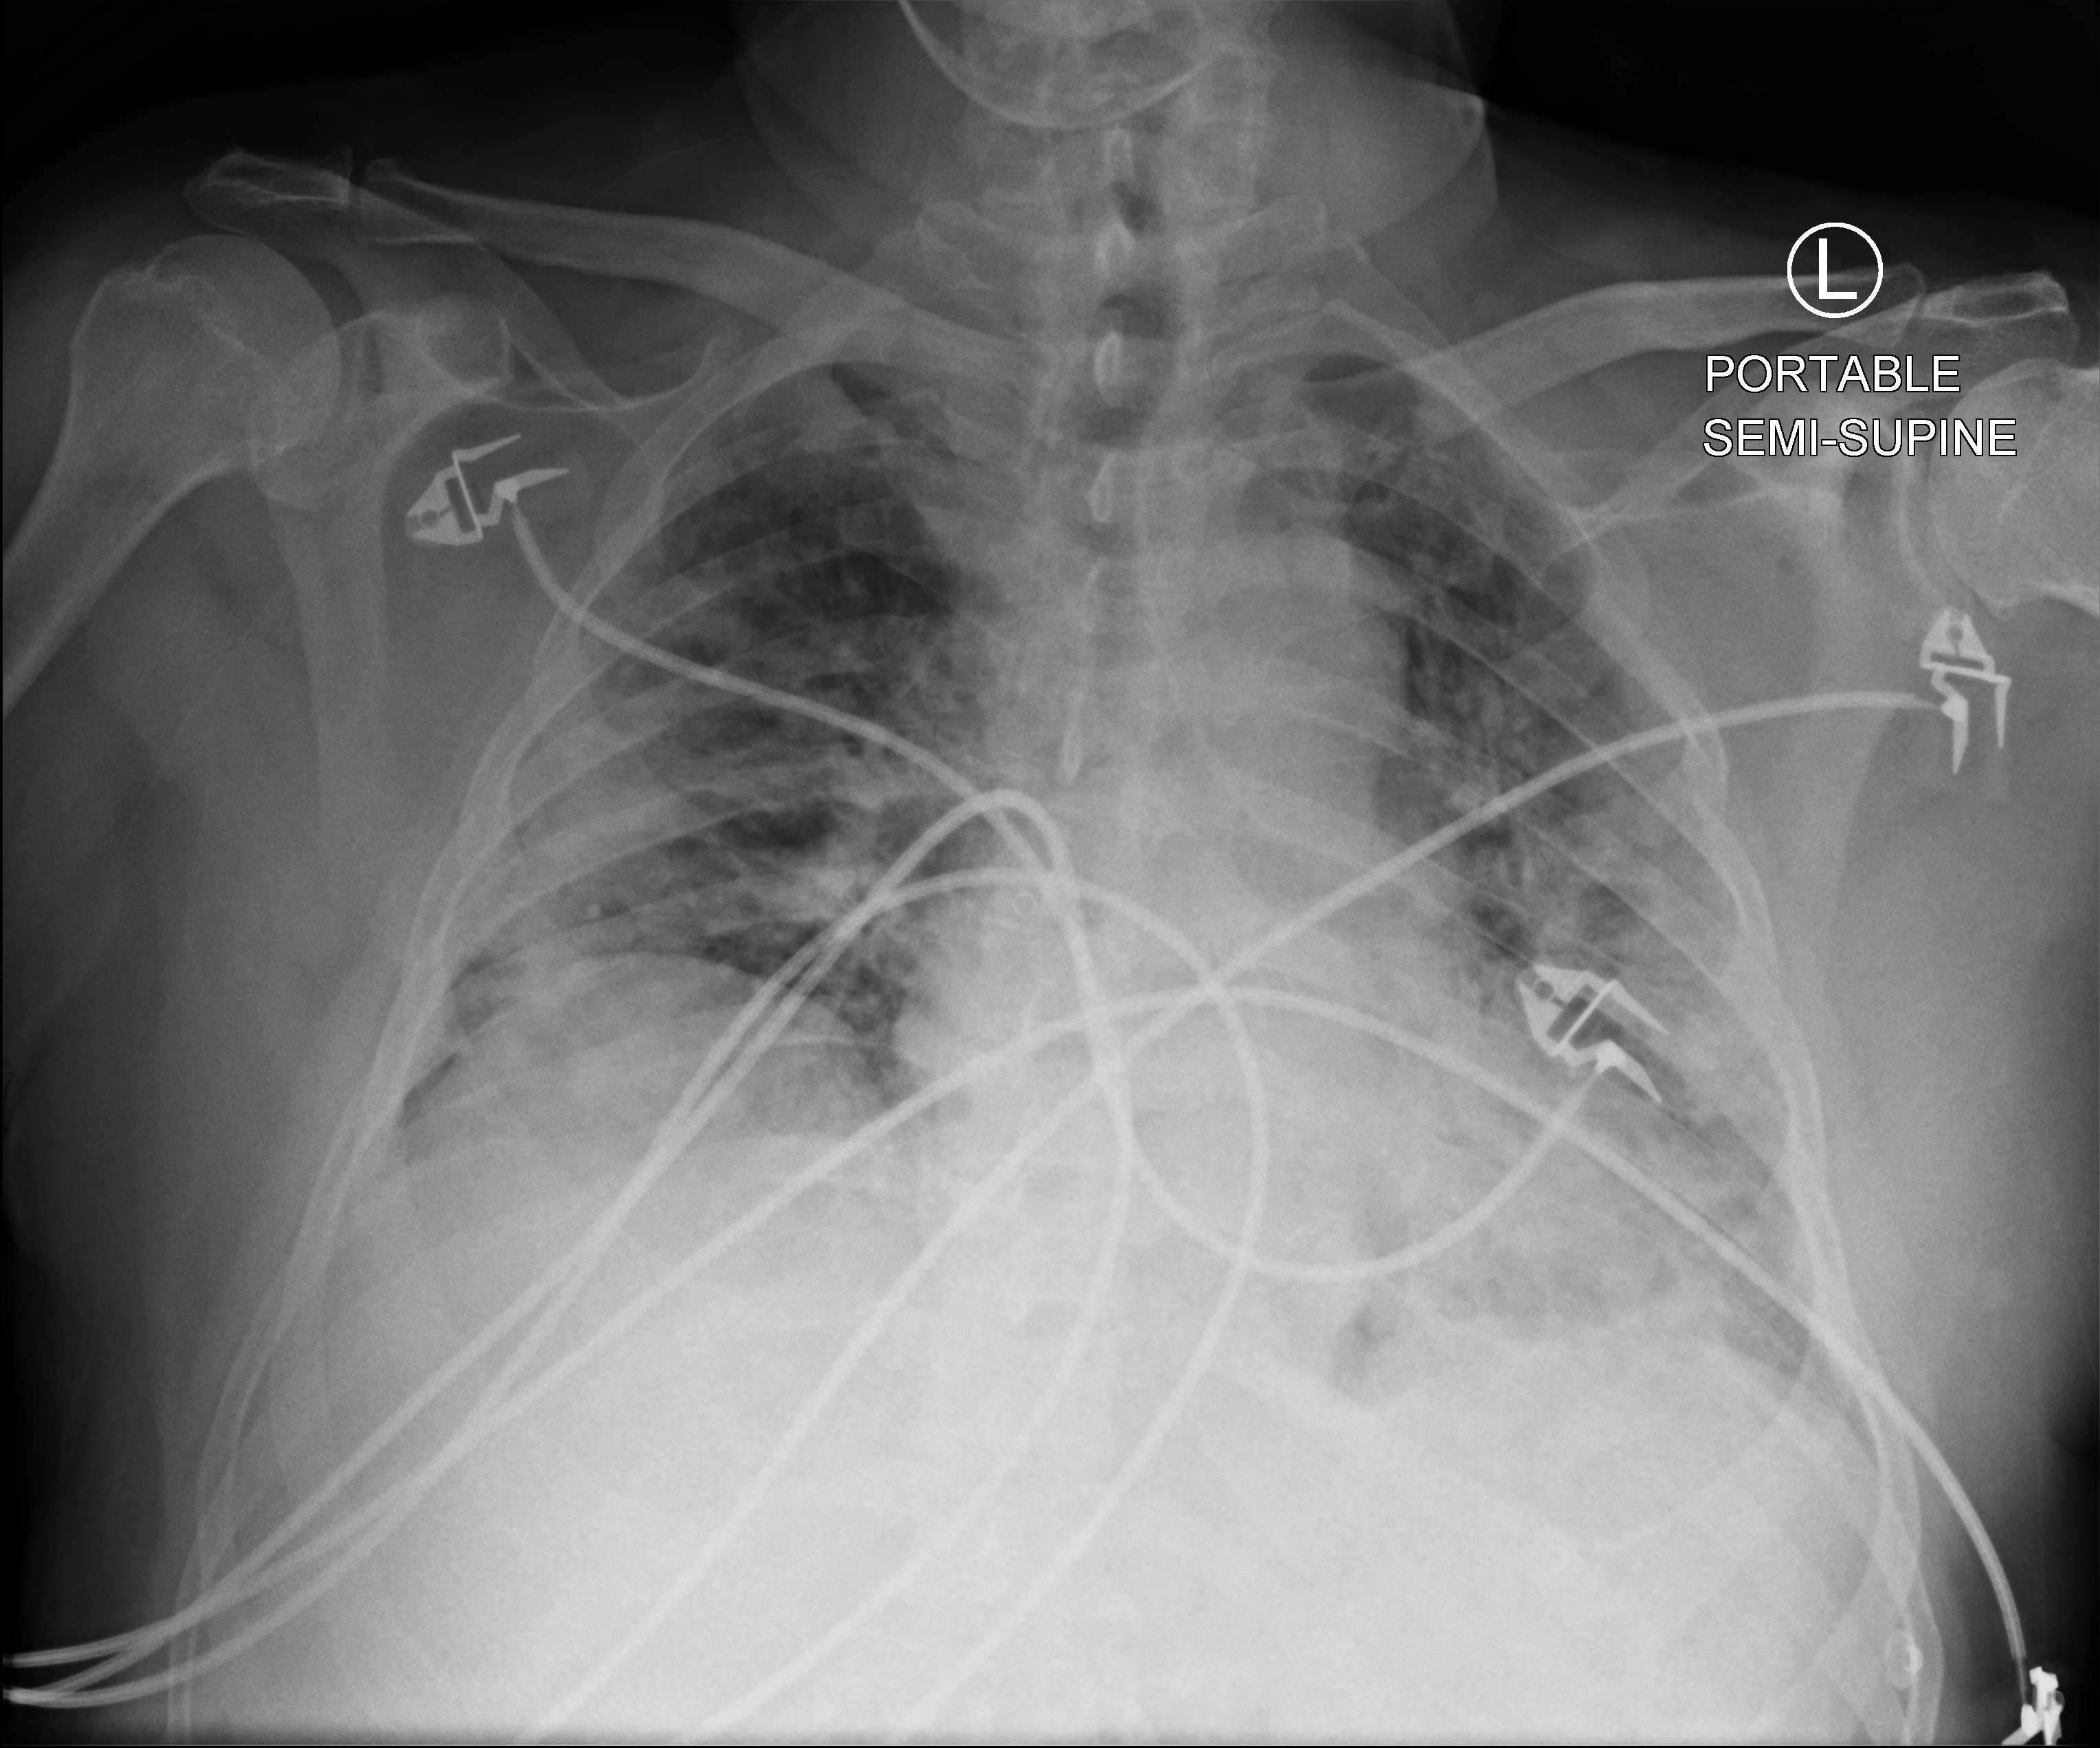
Bedside chest radiograph (computed radiography), anteroposterior (AP) projection. Patient hospitalised with COVID-19; male, aged 60–74 years.
Hospital-stay facts (about this admission, not read from this image; timing relative to this image not recorded):
- COPD (admission record): no
- length of hospital stay: 26 days